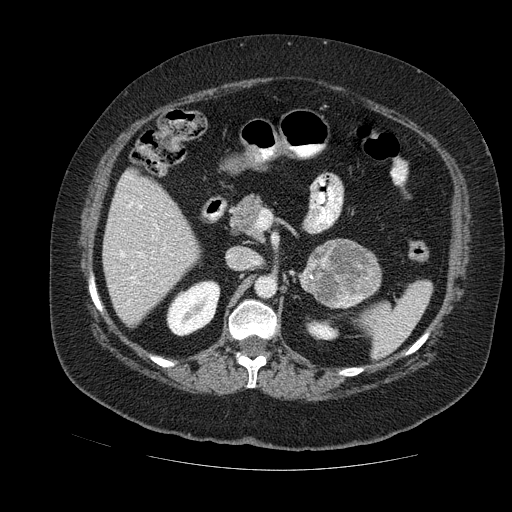
Contrast-enhanced abdominal CT, one axial slice. Position 67 of 121 along the scan axis. Soft-tissue window (W 400 / L 40 HU). 2.5 mm slice thickness. 512 × 512 image matrix, field of view 420 × 420 mm. Female patient. Case-level facts recorded for this patient, not image findings: diagnosis: adrenocortical carcinoma; tumour side: left adrenal.
Structures marked on this image (semi-automatic segmentation, software-assisted and operator-edited):
- mass: box from (x=300, y=240) to (x=379, y=307) px